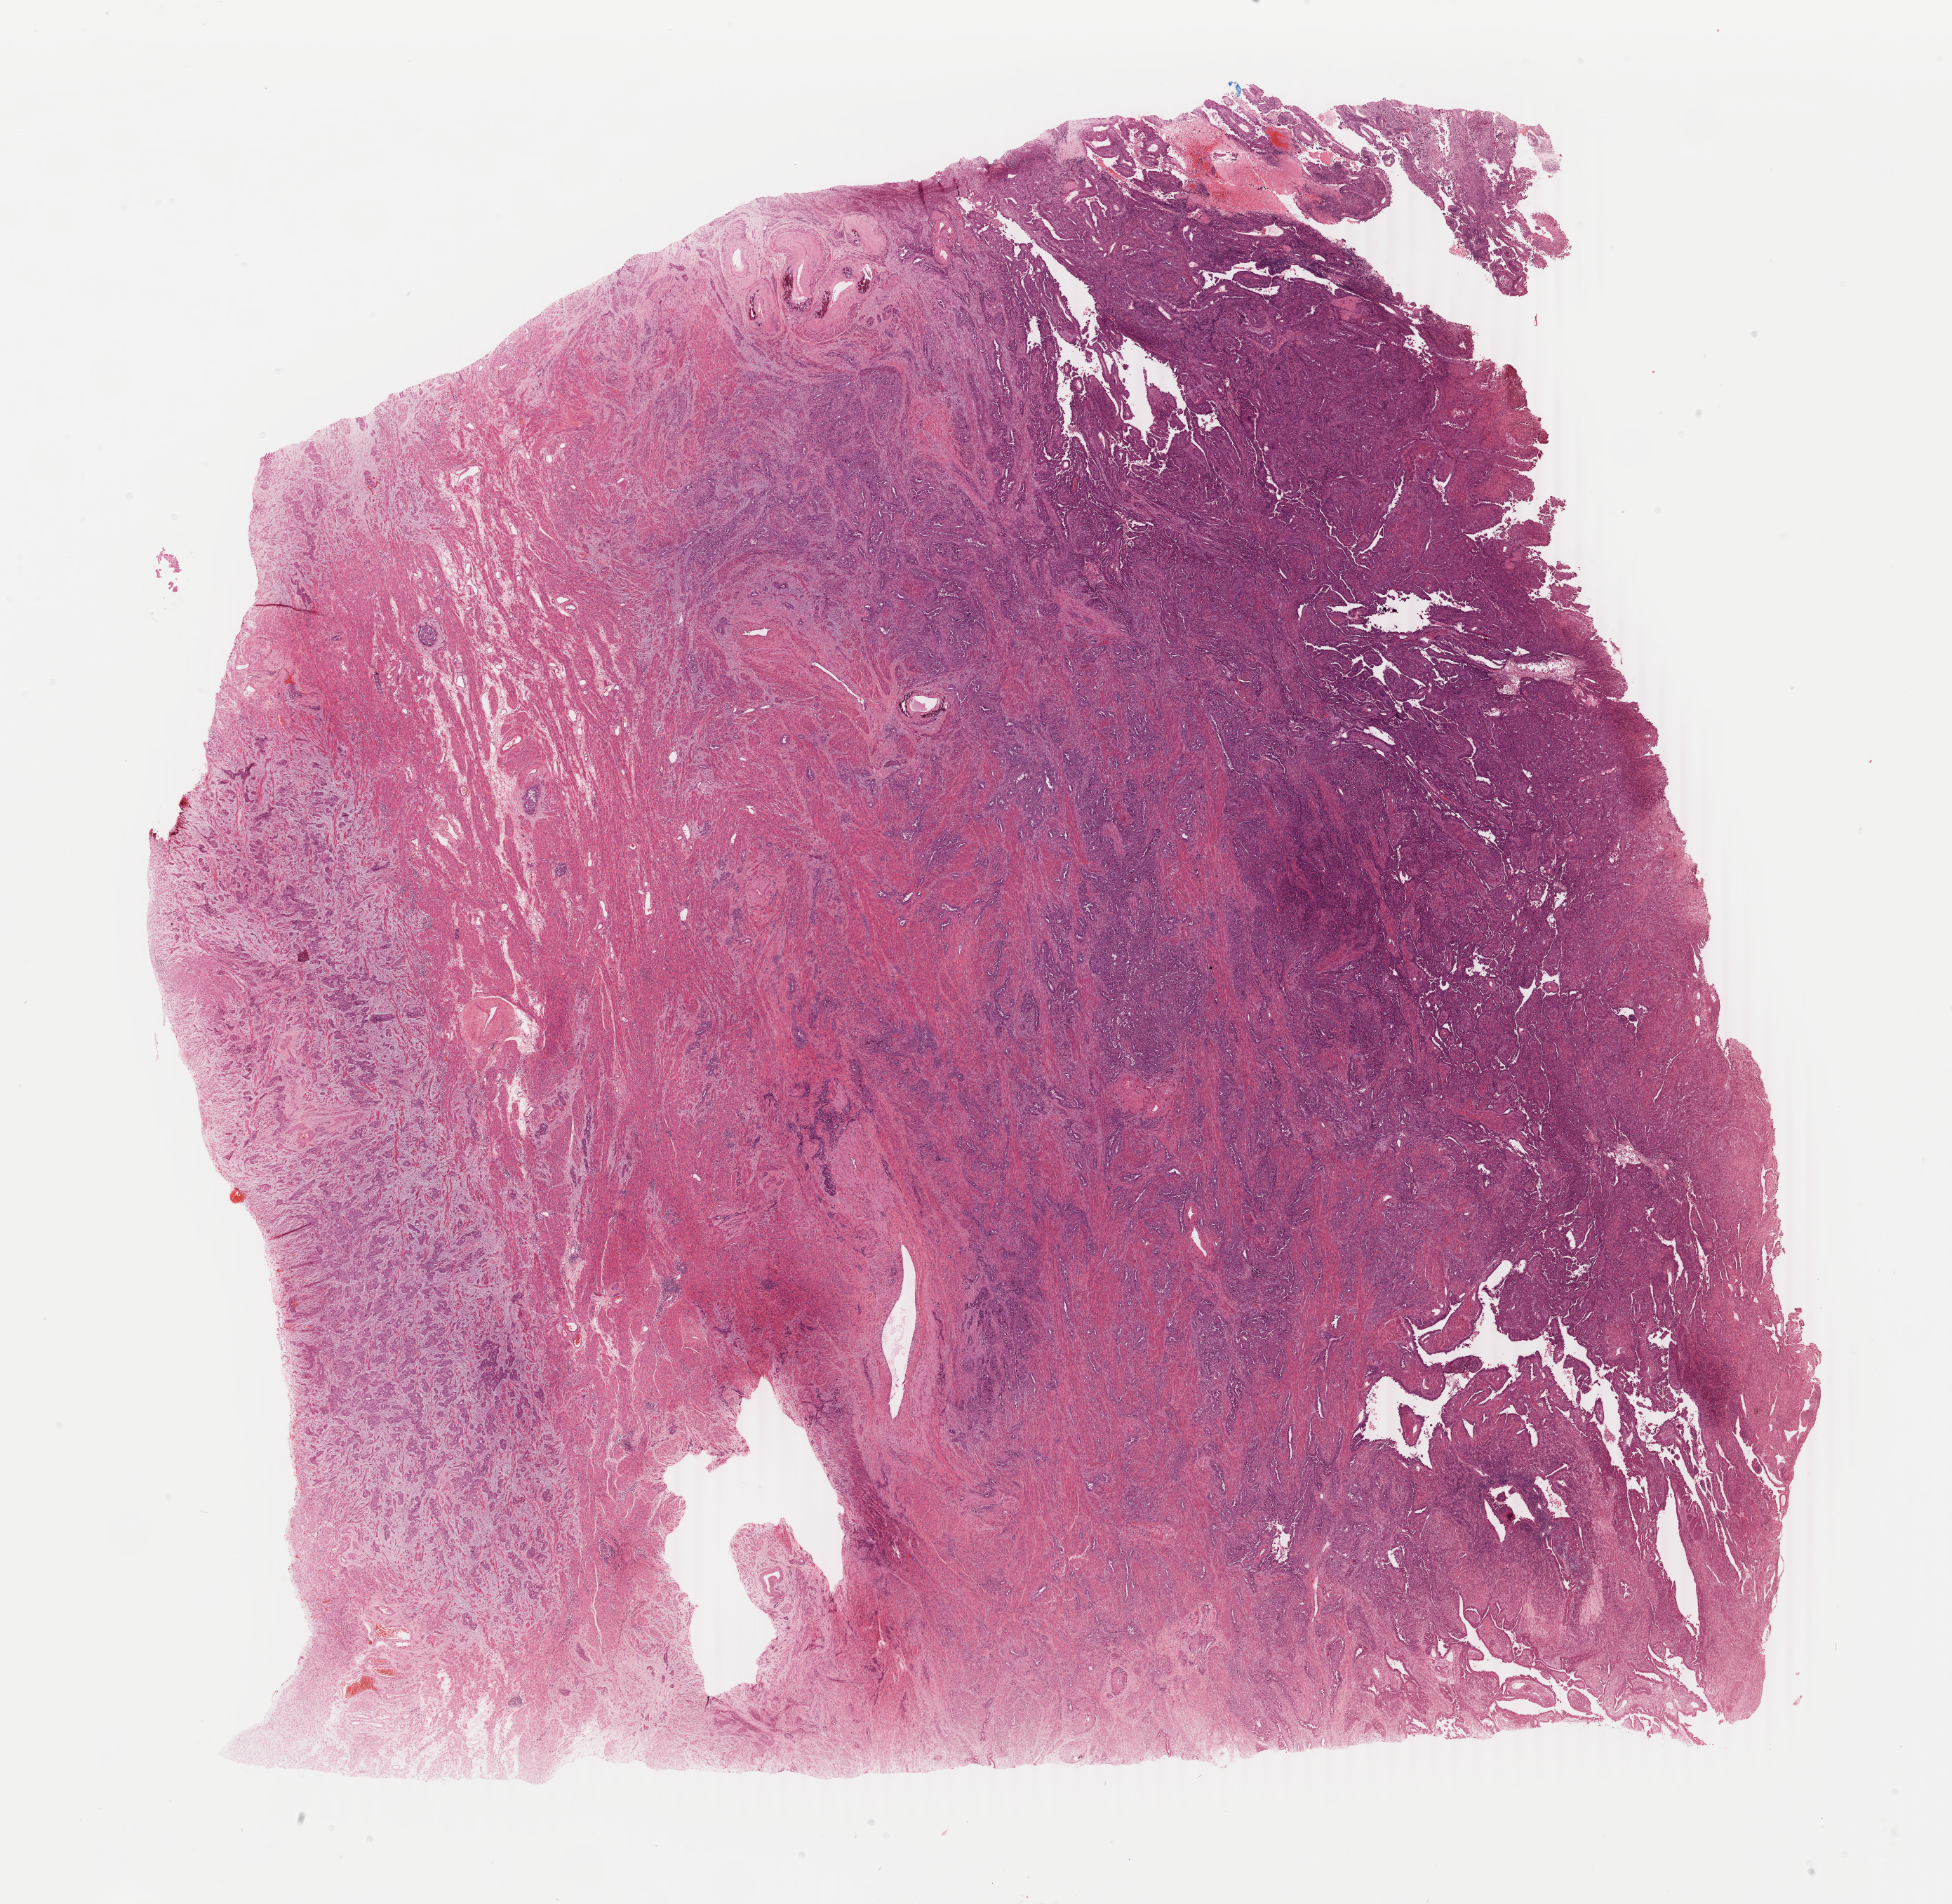
H&E whole-slide image, low-resolution overview of the scanned area, about 22.1 x 21.6 mm. Formalin-fixed paraffin-embedded (FFPE) diagnostic section. Uterus, primary tumour sample. Female, age 86 years at initial diagnosis.
Histologic diagnosis: Serous cystadenocarcinoma, NOS (endometrium).